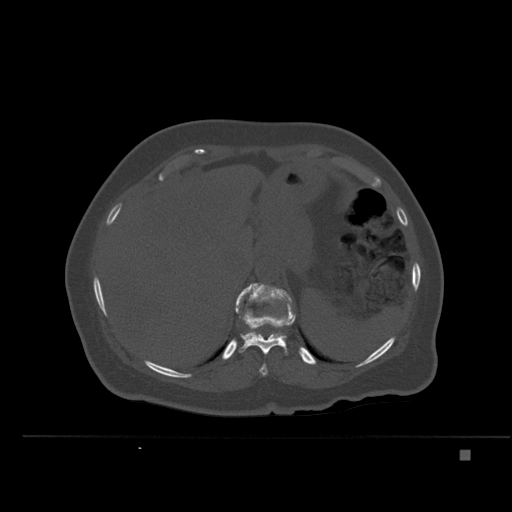
CT including the spine, one axial slice. Position 267 of 477 along the scan axis. Bone window (W 1800 / L 400 HU). 1.5 mm slice thickness. 512 × 512 image matrix. Female patient, age 74 years. From the clinical record (not read from this slice): primary cancer: colon.
Outlined on this slice (semi-automatic segmentation, software-assisted and operator-edited):
- T10 vertebra: bounding box [x1, y1, x2, y2] px = [259, 363, 268, 376]
- T11 vertebra: [236, 291, 296, 355]
- T12 vertebra: [235, 283, 296, 338]